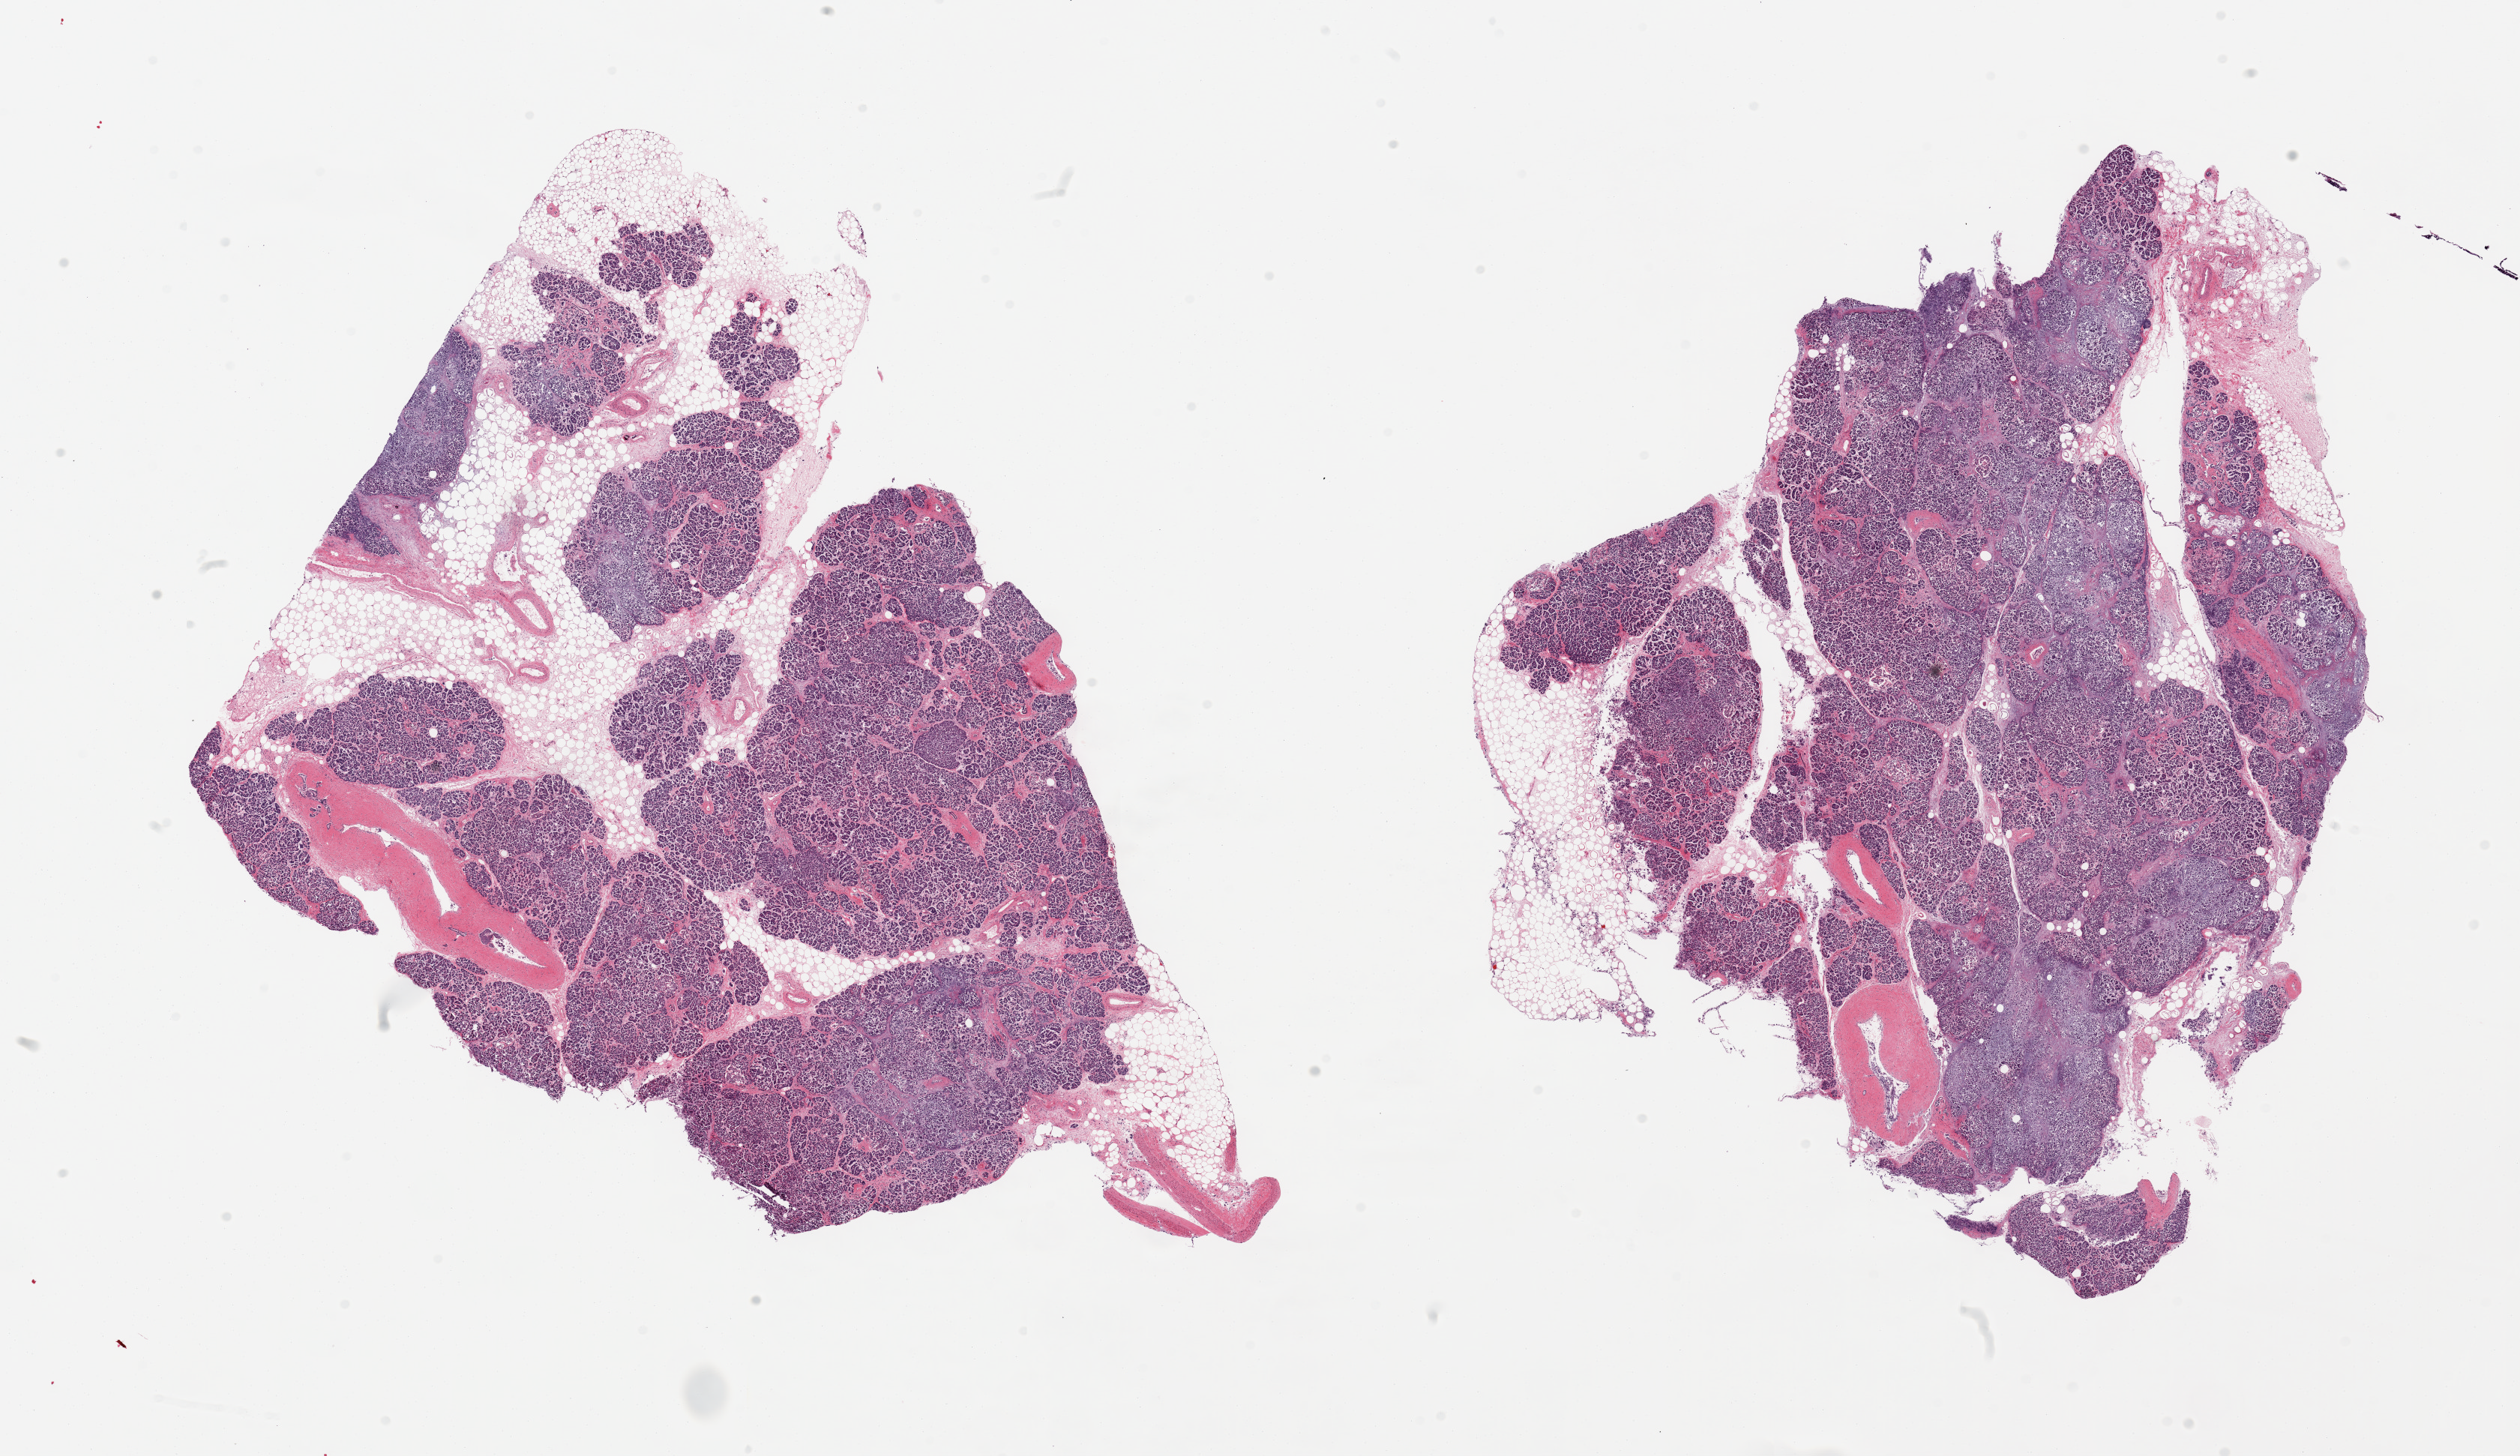
Whole-slide image, hematoxylin and eosin (H&E) stain, brightfield — a low-resolution overview of the entire scanned area, about 26.6 x 15.4 mm, PAXgene-fixed, paraffin-embedded tissue, target tissue: pancreas, donor tissue sample. Donor: male.
• pathologist's review note for this sample: 2 pieces, moderately advanced saponification, rare Islets still visible